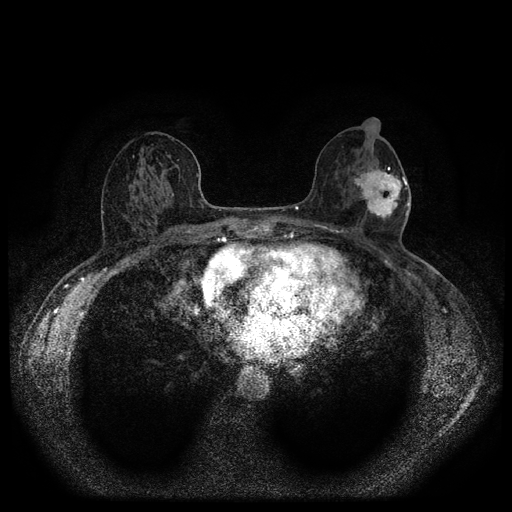
Breast MRI (dynamic contrast-enhanced, multi-phase), one axial slice. Position 51 of 116 along the scan axis. Dynamic contrast-enhanced series, time point 2 of 5 at this slice position (early post-contrast). 1.5 T. TE 2.7 ms, TR 5.4 ms. 512 × 512 image matrix, field of view 330 × 330 mm. Female patient, age 56 years.
Annotated regions visible in this slice (semi-automatic segmentation, software-assisted and operator-edited):
- breast lesion (labelled 'tumour' in the annotation; benign lesions carry a separate 'benign' label): bounding box (x1, y1, x2, y2) in pixels: (353, 165, 405, 223)